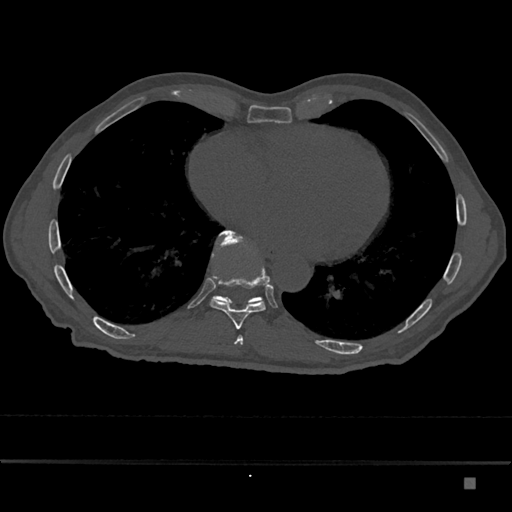
CT including the spine, one axial slice. Slice 788 of 797 in the series (ordered by position). 120 kVp. Bone window (W 1800 / L 400 HU). 0.5 mm slice thickness. 512 × 512 image matrix. Male patient, age 72 years. From the clinical record (not read from this slice): primary cancer: prostate.
Annotated regions visible in this slice (semi-automatically segmented with operator editing):
- T10 vertebra: bounding box [x1, y1, x2, y2] px = [212, 230, 263, 304]
- T9 vertebra: [210, 230, 270, 330]